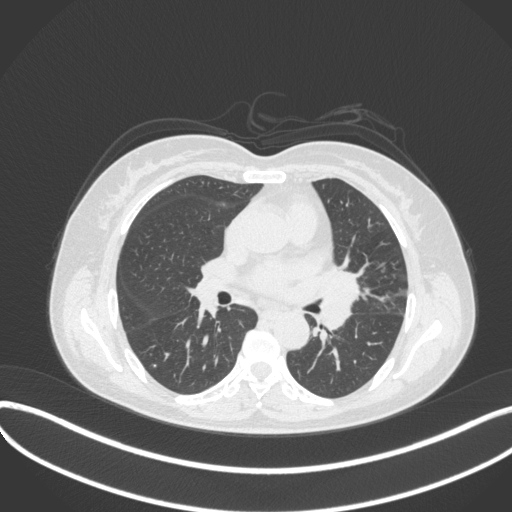
Chest CT, one axial slice; slice 190 of 373 in the series (ordered by position); lung window (W 1500 / L -600 HU); 1 mm slice thickness; 512 × 512 image matrix. Patient: female, 54 years. From the clinical record (not read from this slice): clinical TNM (as recorded): T2a N1 M0; histopathological grade: G3.
Outlined on this slice (bounding box drawn by a radiologist):
- lung tumour (recorded histology: small cell carcinoma): box from (x=318, y=264) to (x=363, y=333) px